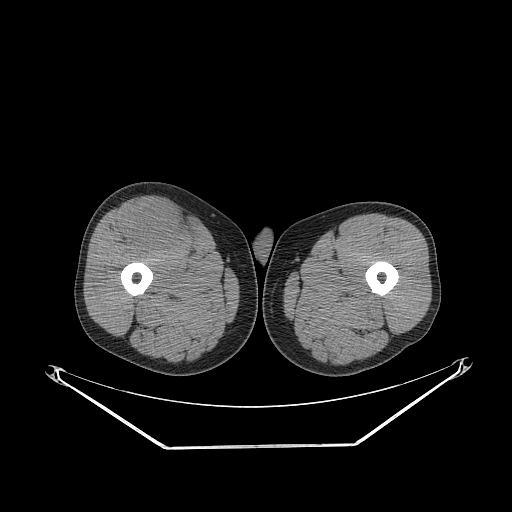
CT of an extremity soft-tissue mass (from a PET/CT study), one axial slice; slice 270 of 311 in the series (ordered by position); 140 kVp; soft-tissue window (W 400 / L 40 HU); 512 × 512 image matrix, field of view 500 × 500 mm. Male patient. Case-level facts recorded for this patient, not image findings: histological type: pleiomorphic leiomyosarcoma; grade: intermediate; site of the primary tumour: right thigh.
Structures marked on this image (expert contour drawn on MRI and transferred to this co-registered scan by the dataset authors):
- gross tumour volume including surrounding oedema: bounding box [x1, y1, x2, y2] px = [121, 203, 184, 252]
- gross tumour volume (mass): [121, 206, 184, 252]